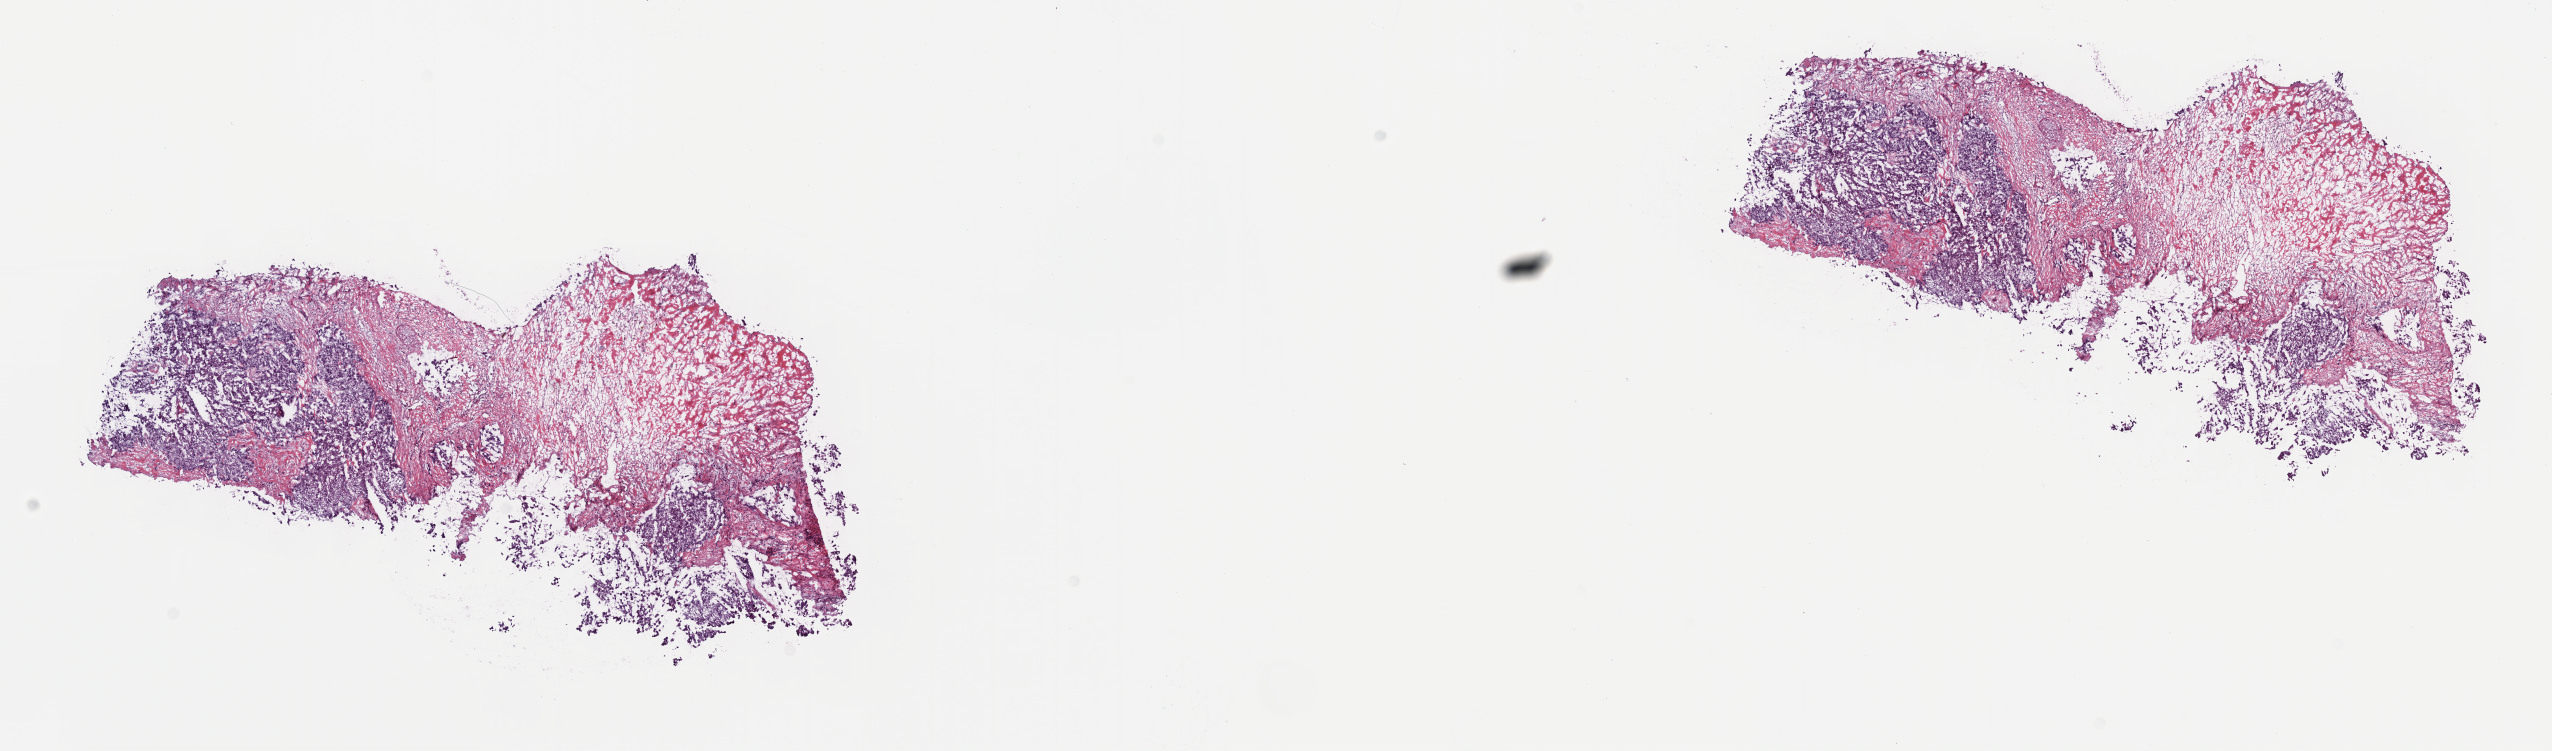
Digitized H&E tissue section (whole slide), a low-resolution overview of the entire scanned area, about 20.6 x 6.1 mm (slide scanned at 40x), frozen section from the top of the tissue portion, sample: primary tumour, liver. Male, age 68 years at initial diagnosis. Histologic grade: G2 (moderately differentiated). Pathologist review of this section (percent, as recorded): tumour cells 65%, tumour nuclei 65%, normal cells 0%, stromal cells 35%, necrosis 0%. Inflammatory infiltration, as recorded: lymphocyte infiltration 0%, monocyte infiltration 0%, neutrophil infiltration 0%.
Histologic diagnosis: Hepatocellular carcinoma, NOS. AJCC pathologic stage: I (7th edition). TNM: T1 N0 MX.